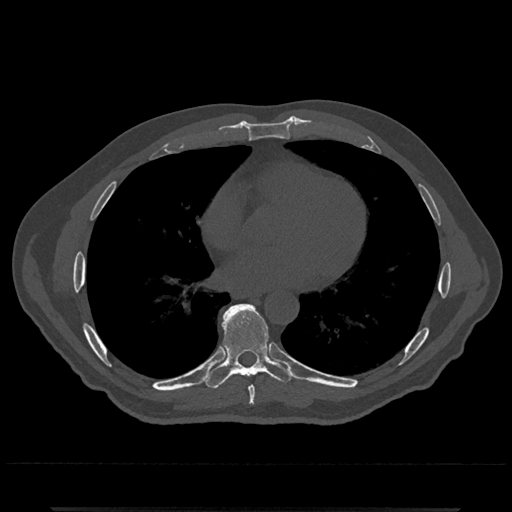
CT including the spine, one axial slice. Position 681 of 797 along the scan axis. 120 kVp. Bone window (W 1800 / L 400 HU). 0.5 mm slice thickness. 512 × 512 image matrix, field of view 393 × 393 mm. Patient: male, 67 years. From the clinical record (not read from this slice): primary cancer: prostate.
Outlined on this slice (semi-automatically segmented with operator editing):
- T7 vertebra: box from (x=249, y=386) to (x=255, y=405) px
- T8 vertebra: (x=201, y=304)–(x=296, y=389)